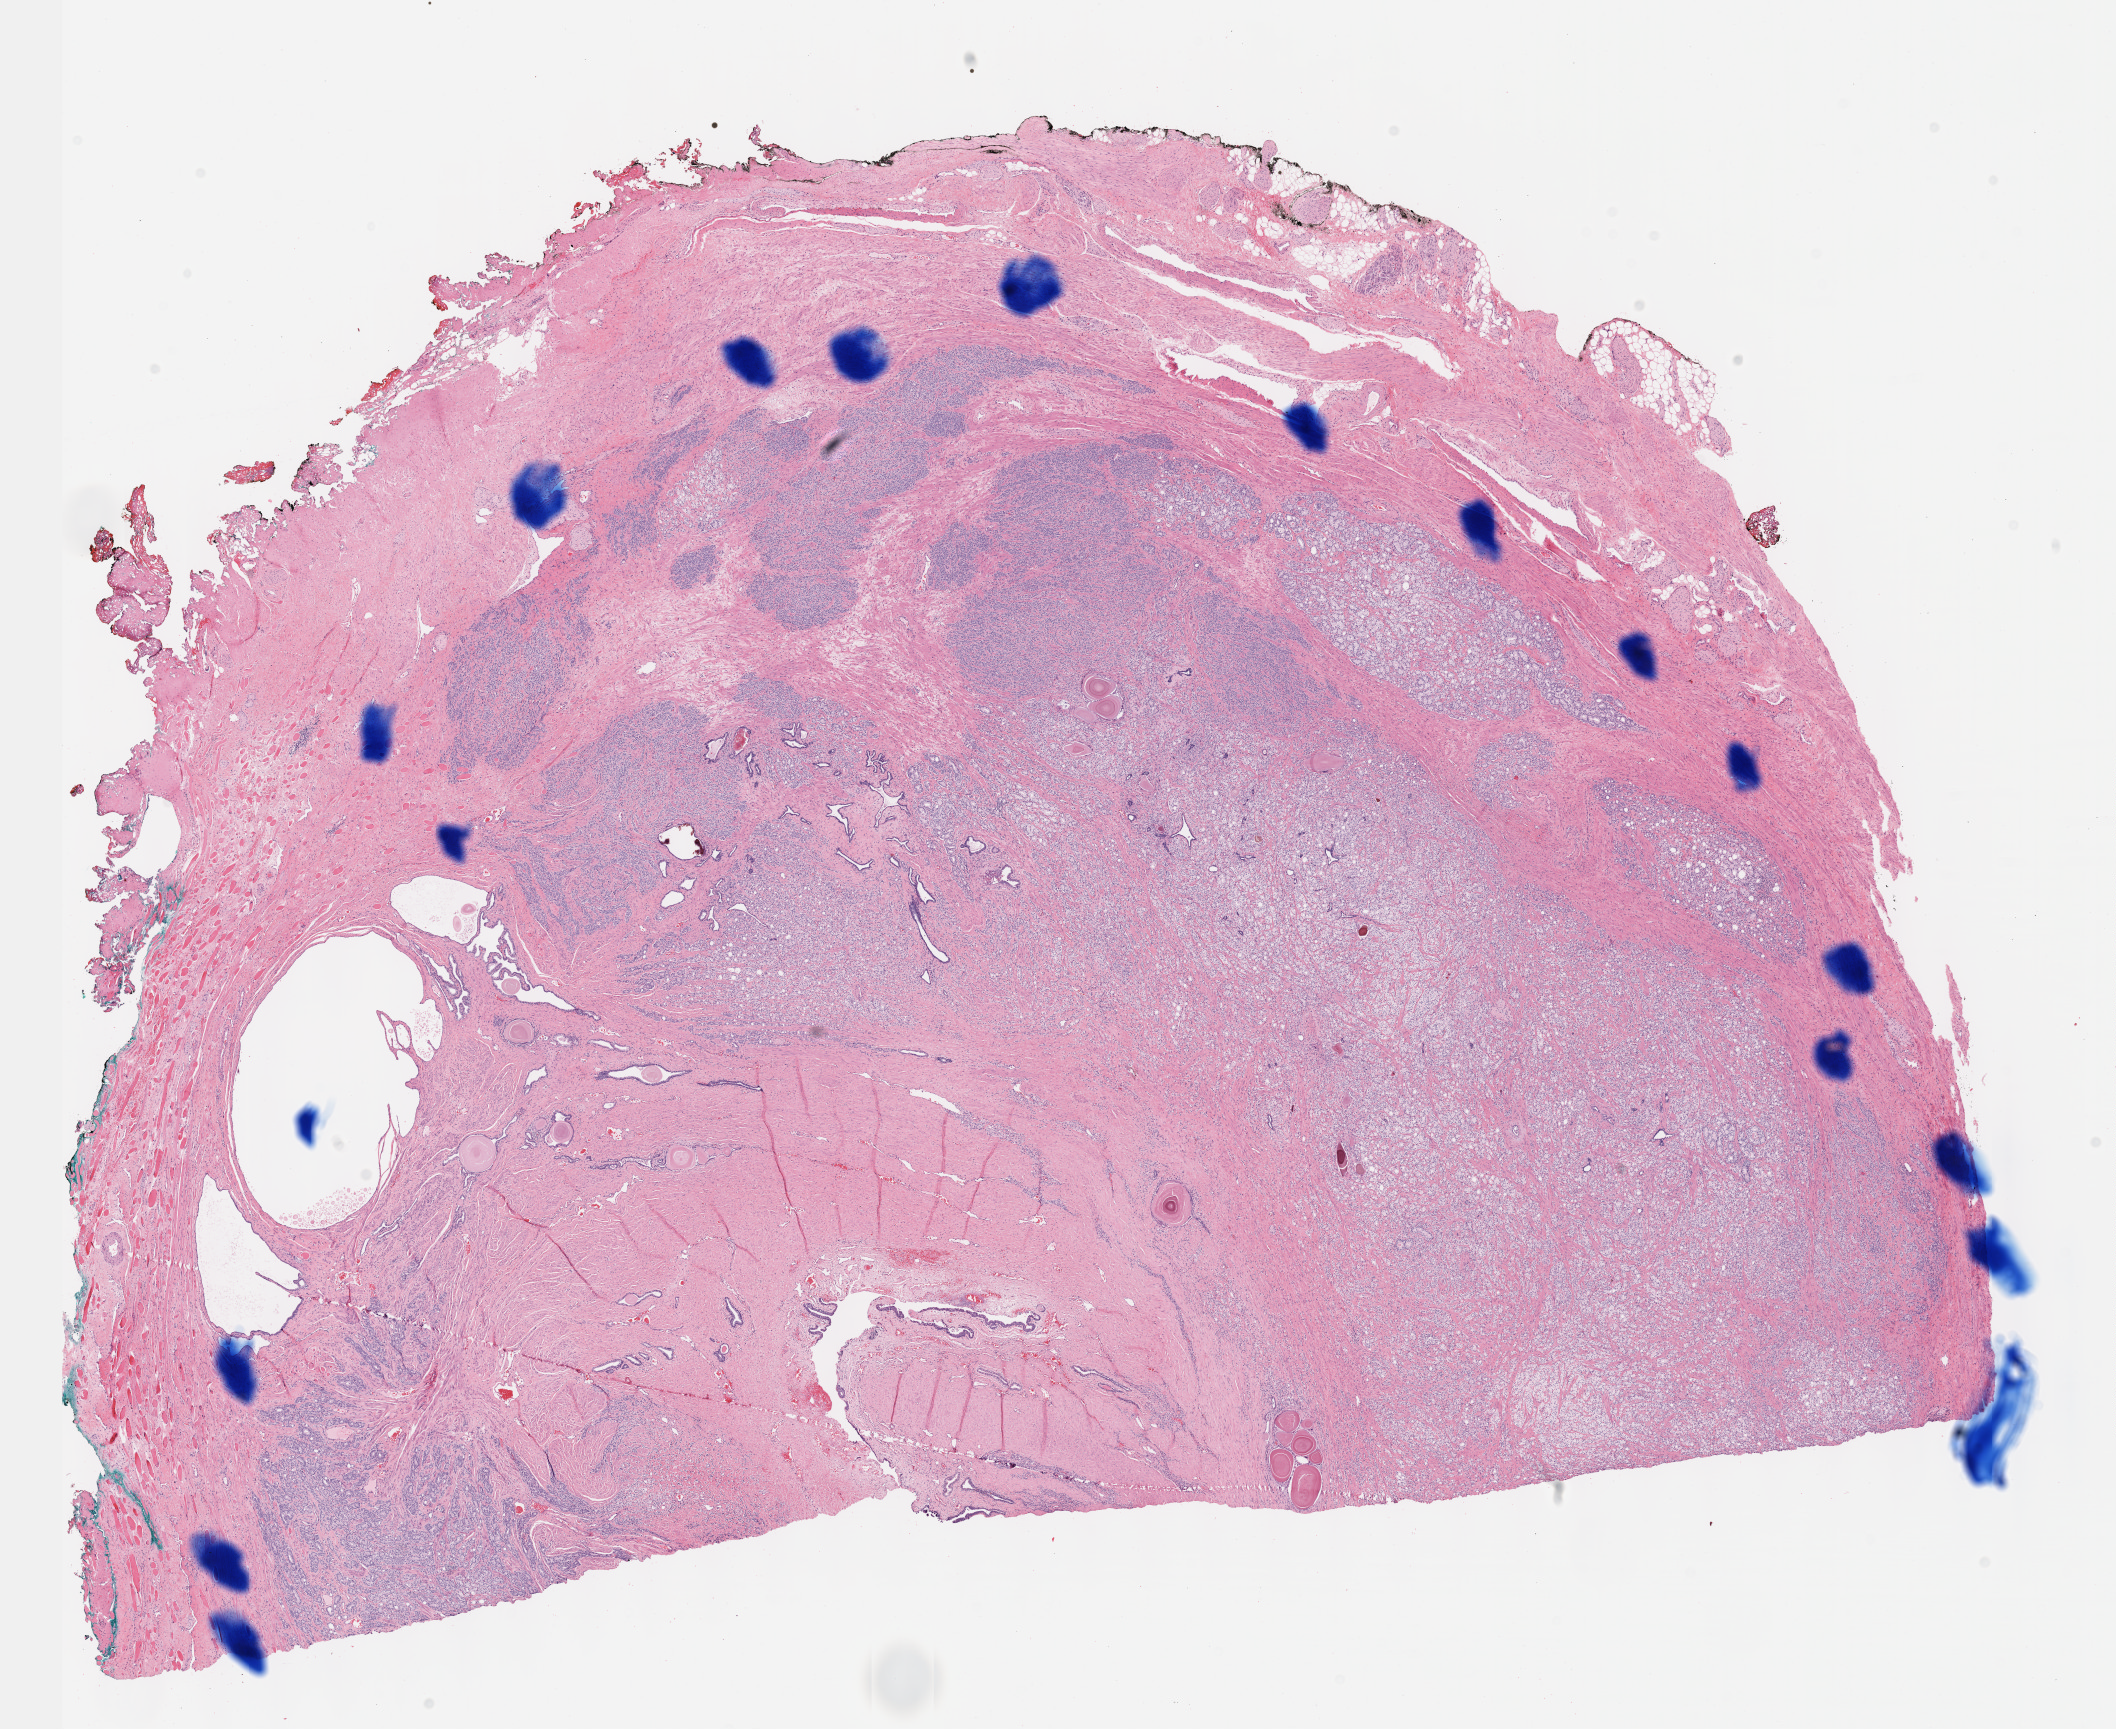
Hematoxylin and eosin (H&E) stained whole-slide image — shown as a low-resolution overview of the whole scanned area (about 17.1 x 14.0 mm). Formalin-fixed paraffin-embedded (FFPE) diagnostic section. Primary tumour sample from the prostate. Patient: male, age at initial diagnosis 68 years. Gleason score: 8 (4+4).
Pathologic diagnosis: Adenocarcinoma, NOS (prostate gland). Laterality: bilateral.